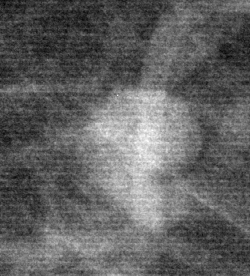
Cropped region of a digitized screen-film mammogram centred on a radiologist-marked abnormality, right breast, CC view, BI-RADS breast density category 2 (scale 1–4).
- Mass, shape lobulated, margins circumscribed; BI-RADS assessment category 2; subtlety rating 5 on a 1 (subtle) to 5 (obvious) scale; benign without callback (not worked up further).